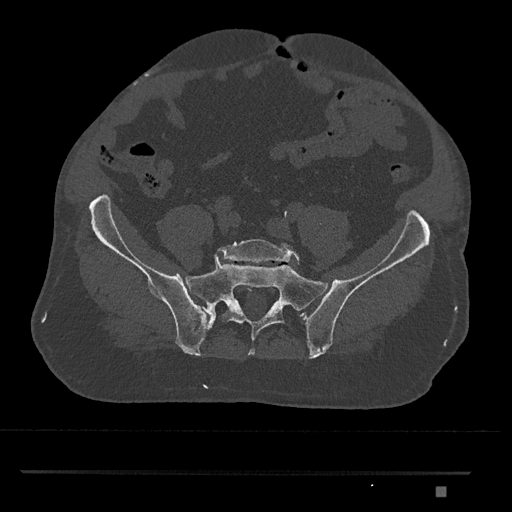
CT including the spine, one axial slice; position 510 of 1134 along the scan axis; 120 kVp; bone window (W 1800 / L 400 HU); 0.5 mm slice thickness; 512 × 512 image matrix, field of view 429 × 429 mm. Patient: male, 65 years. Case-level facts recorded for this patient, not image findings: primary cancer: prostate.
Annotated regions visible in this slice (semi-automatically segmented with operator editing):
- L5 vertebra: bounding box <217,239,300,265> (left, top, right, bottom; pixels)